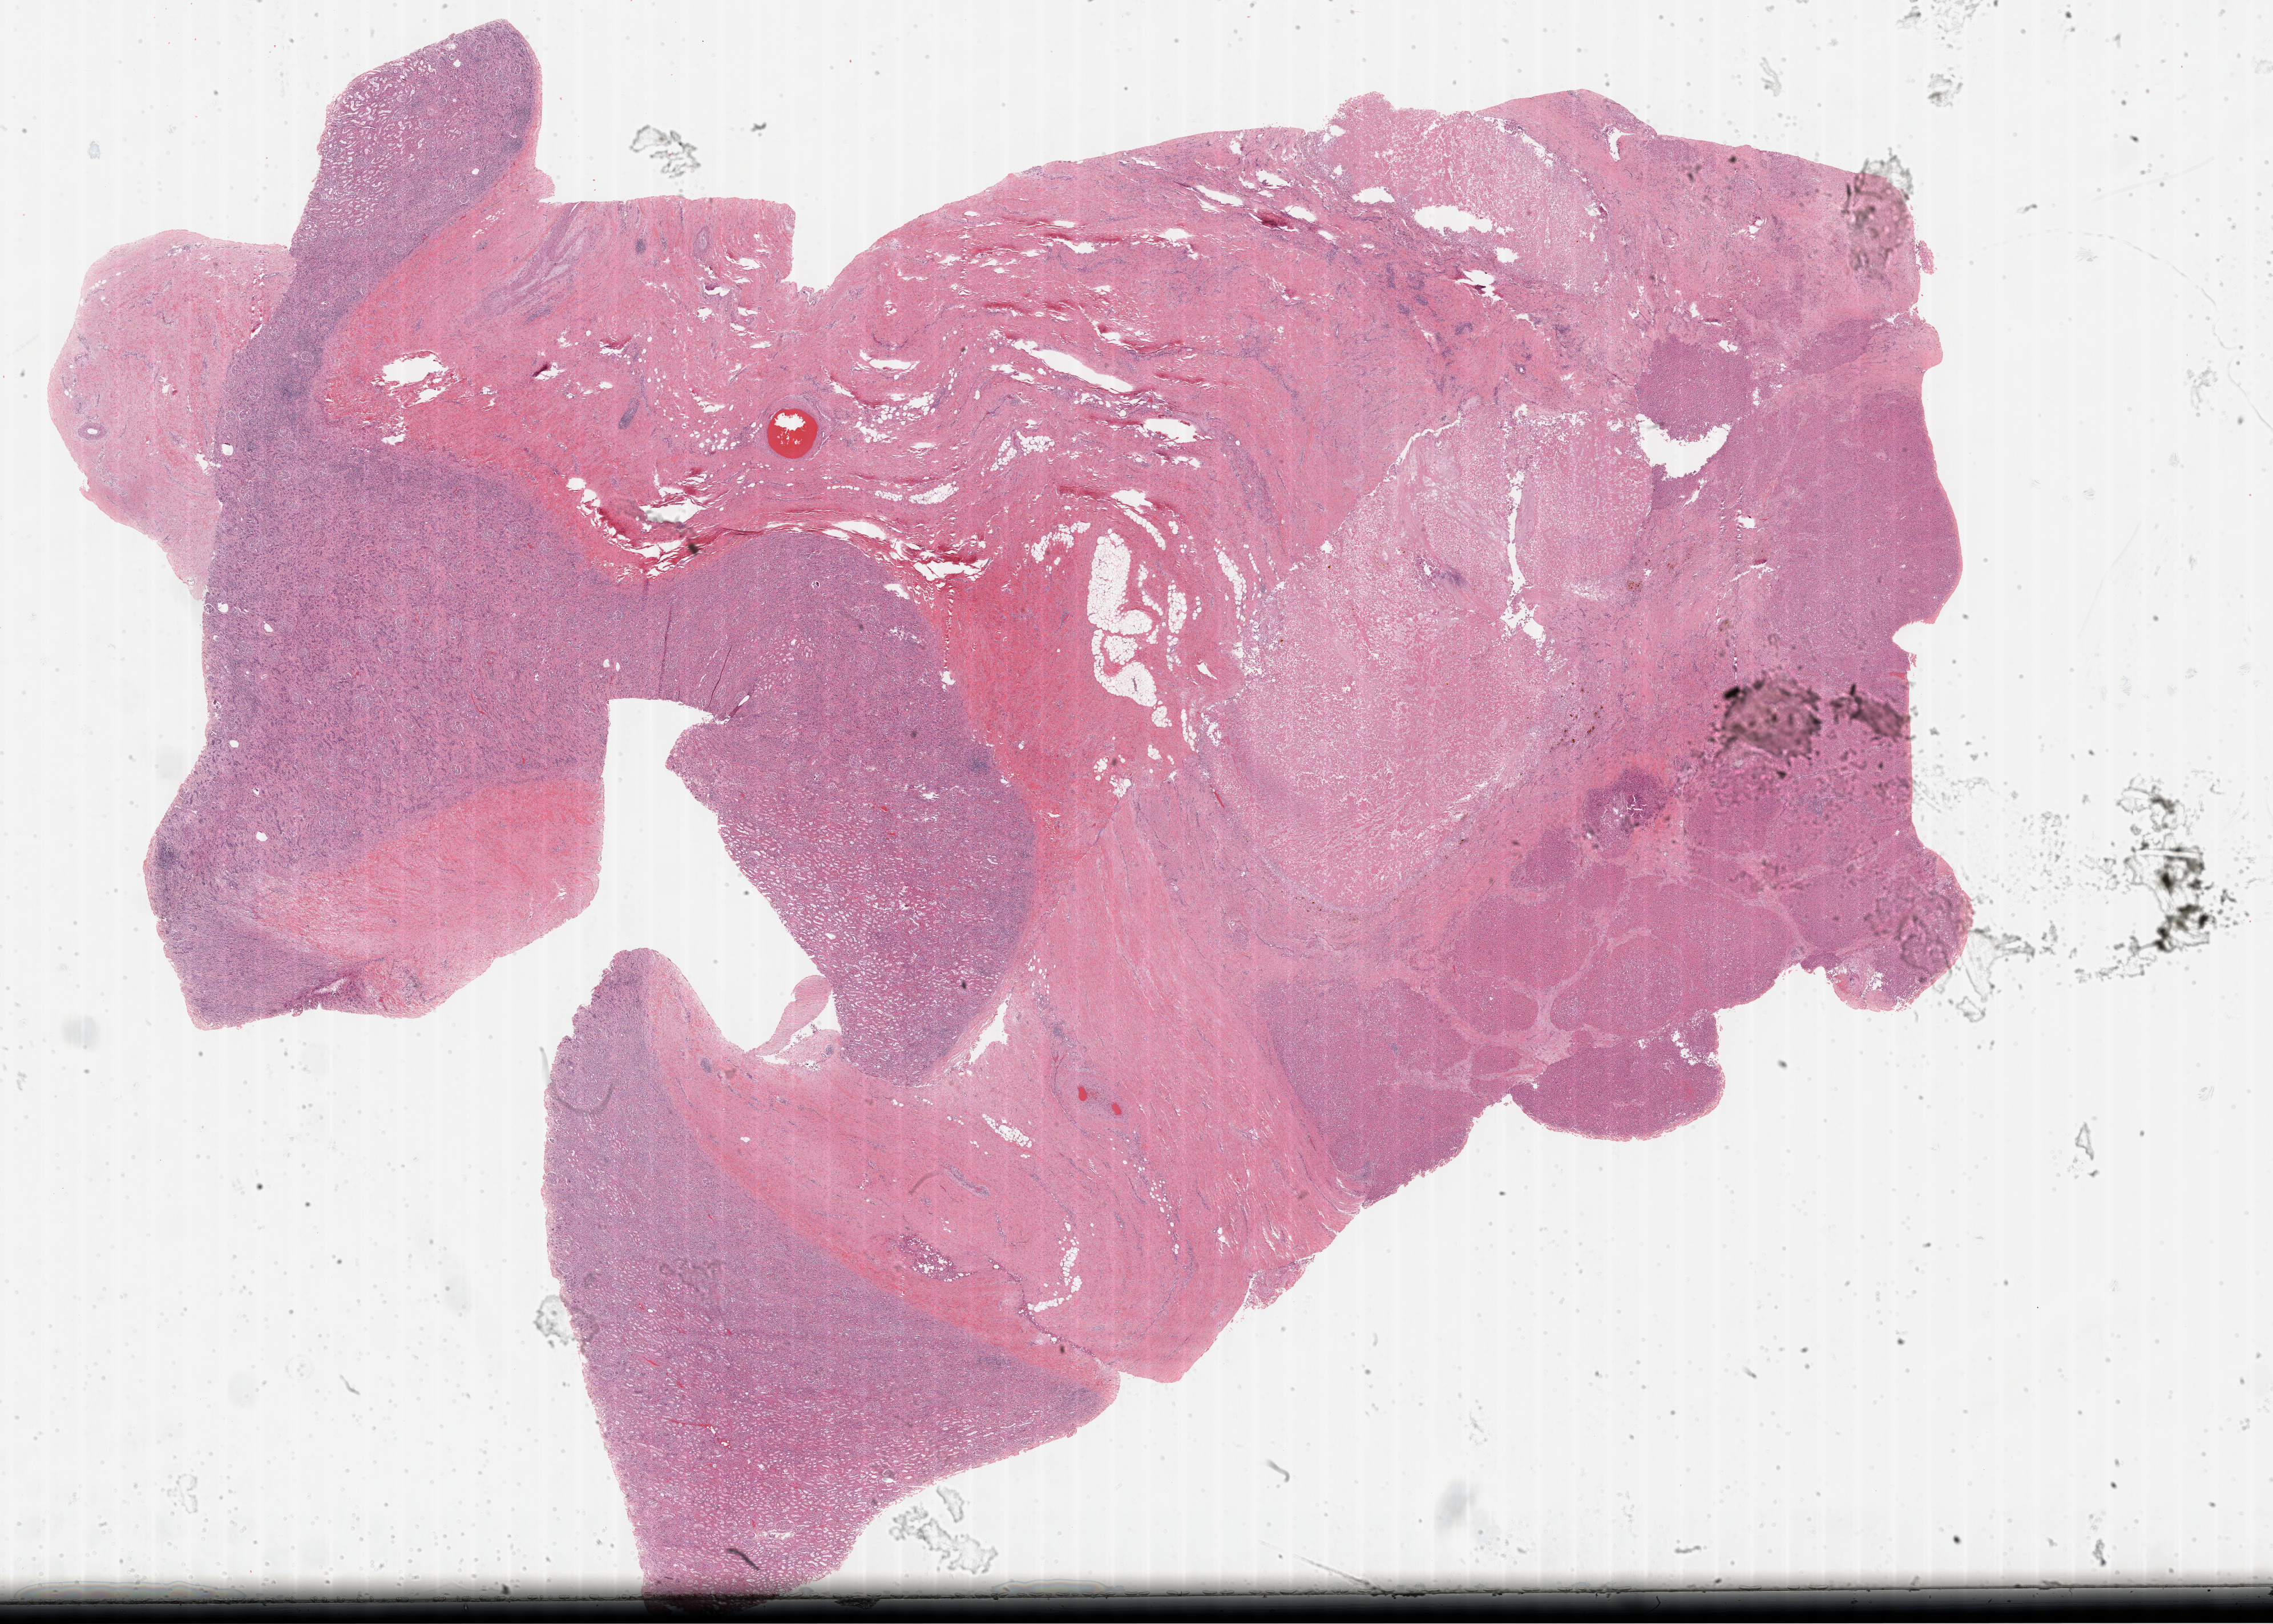
Whole-slide histology image, H&E — shown as a low-resolution overview of the whole scanned area (about 32.2 x 23.0 mm), formalin-fixed paraffin-embedded (FFPE) diagnostic section, sample: primary tumour, adrenal cortex. Male patient; age at initial diagnosis 53 years.
- diagnosis: Adrenal cortical carcinoma